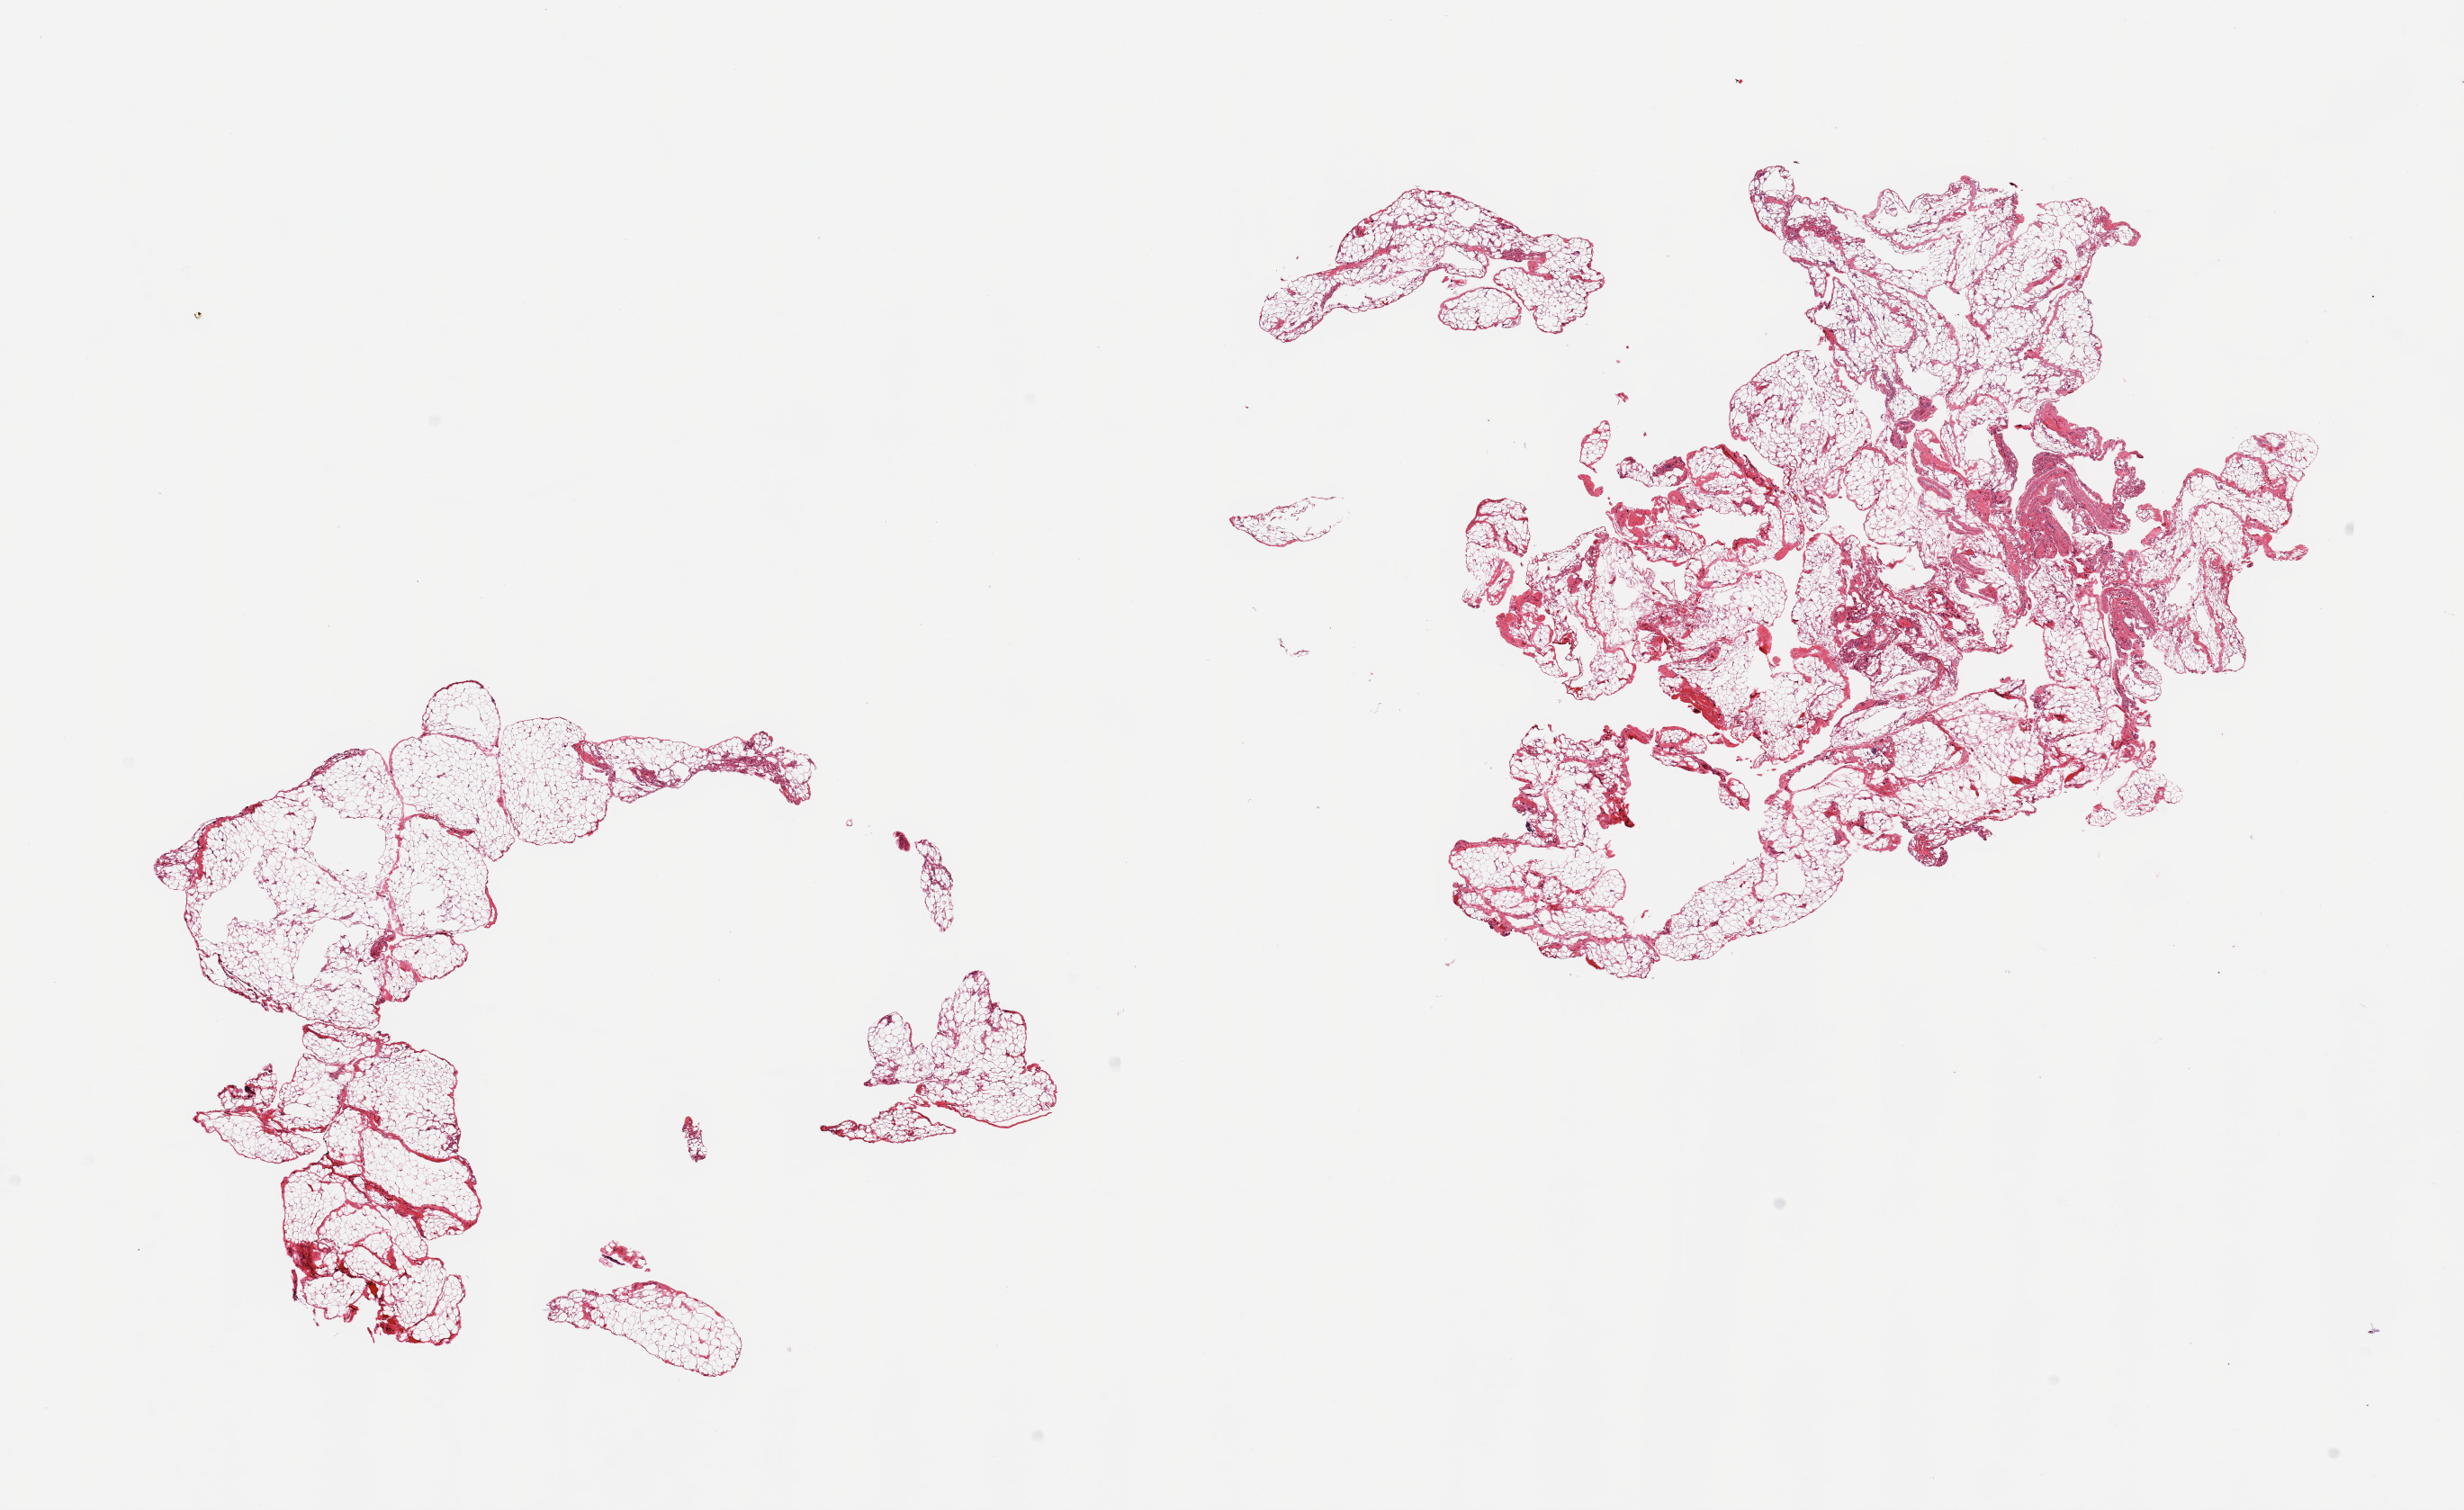
Digitized H&E-stained section, a low-resolution overview of the entire scanned area, about 21.7 x 13.3 mm (slide scanned at 20x); PAXgene-fixed paraffin-embedded (PFPE) section; sampled site (target tissue): omentum; donor tissue sample. Male donor.
- review note (as recorded): 2 pieces, fascia/vascular elemetents are ~20% of tissue